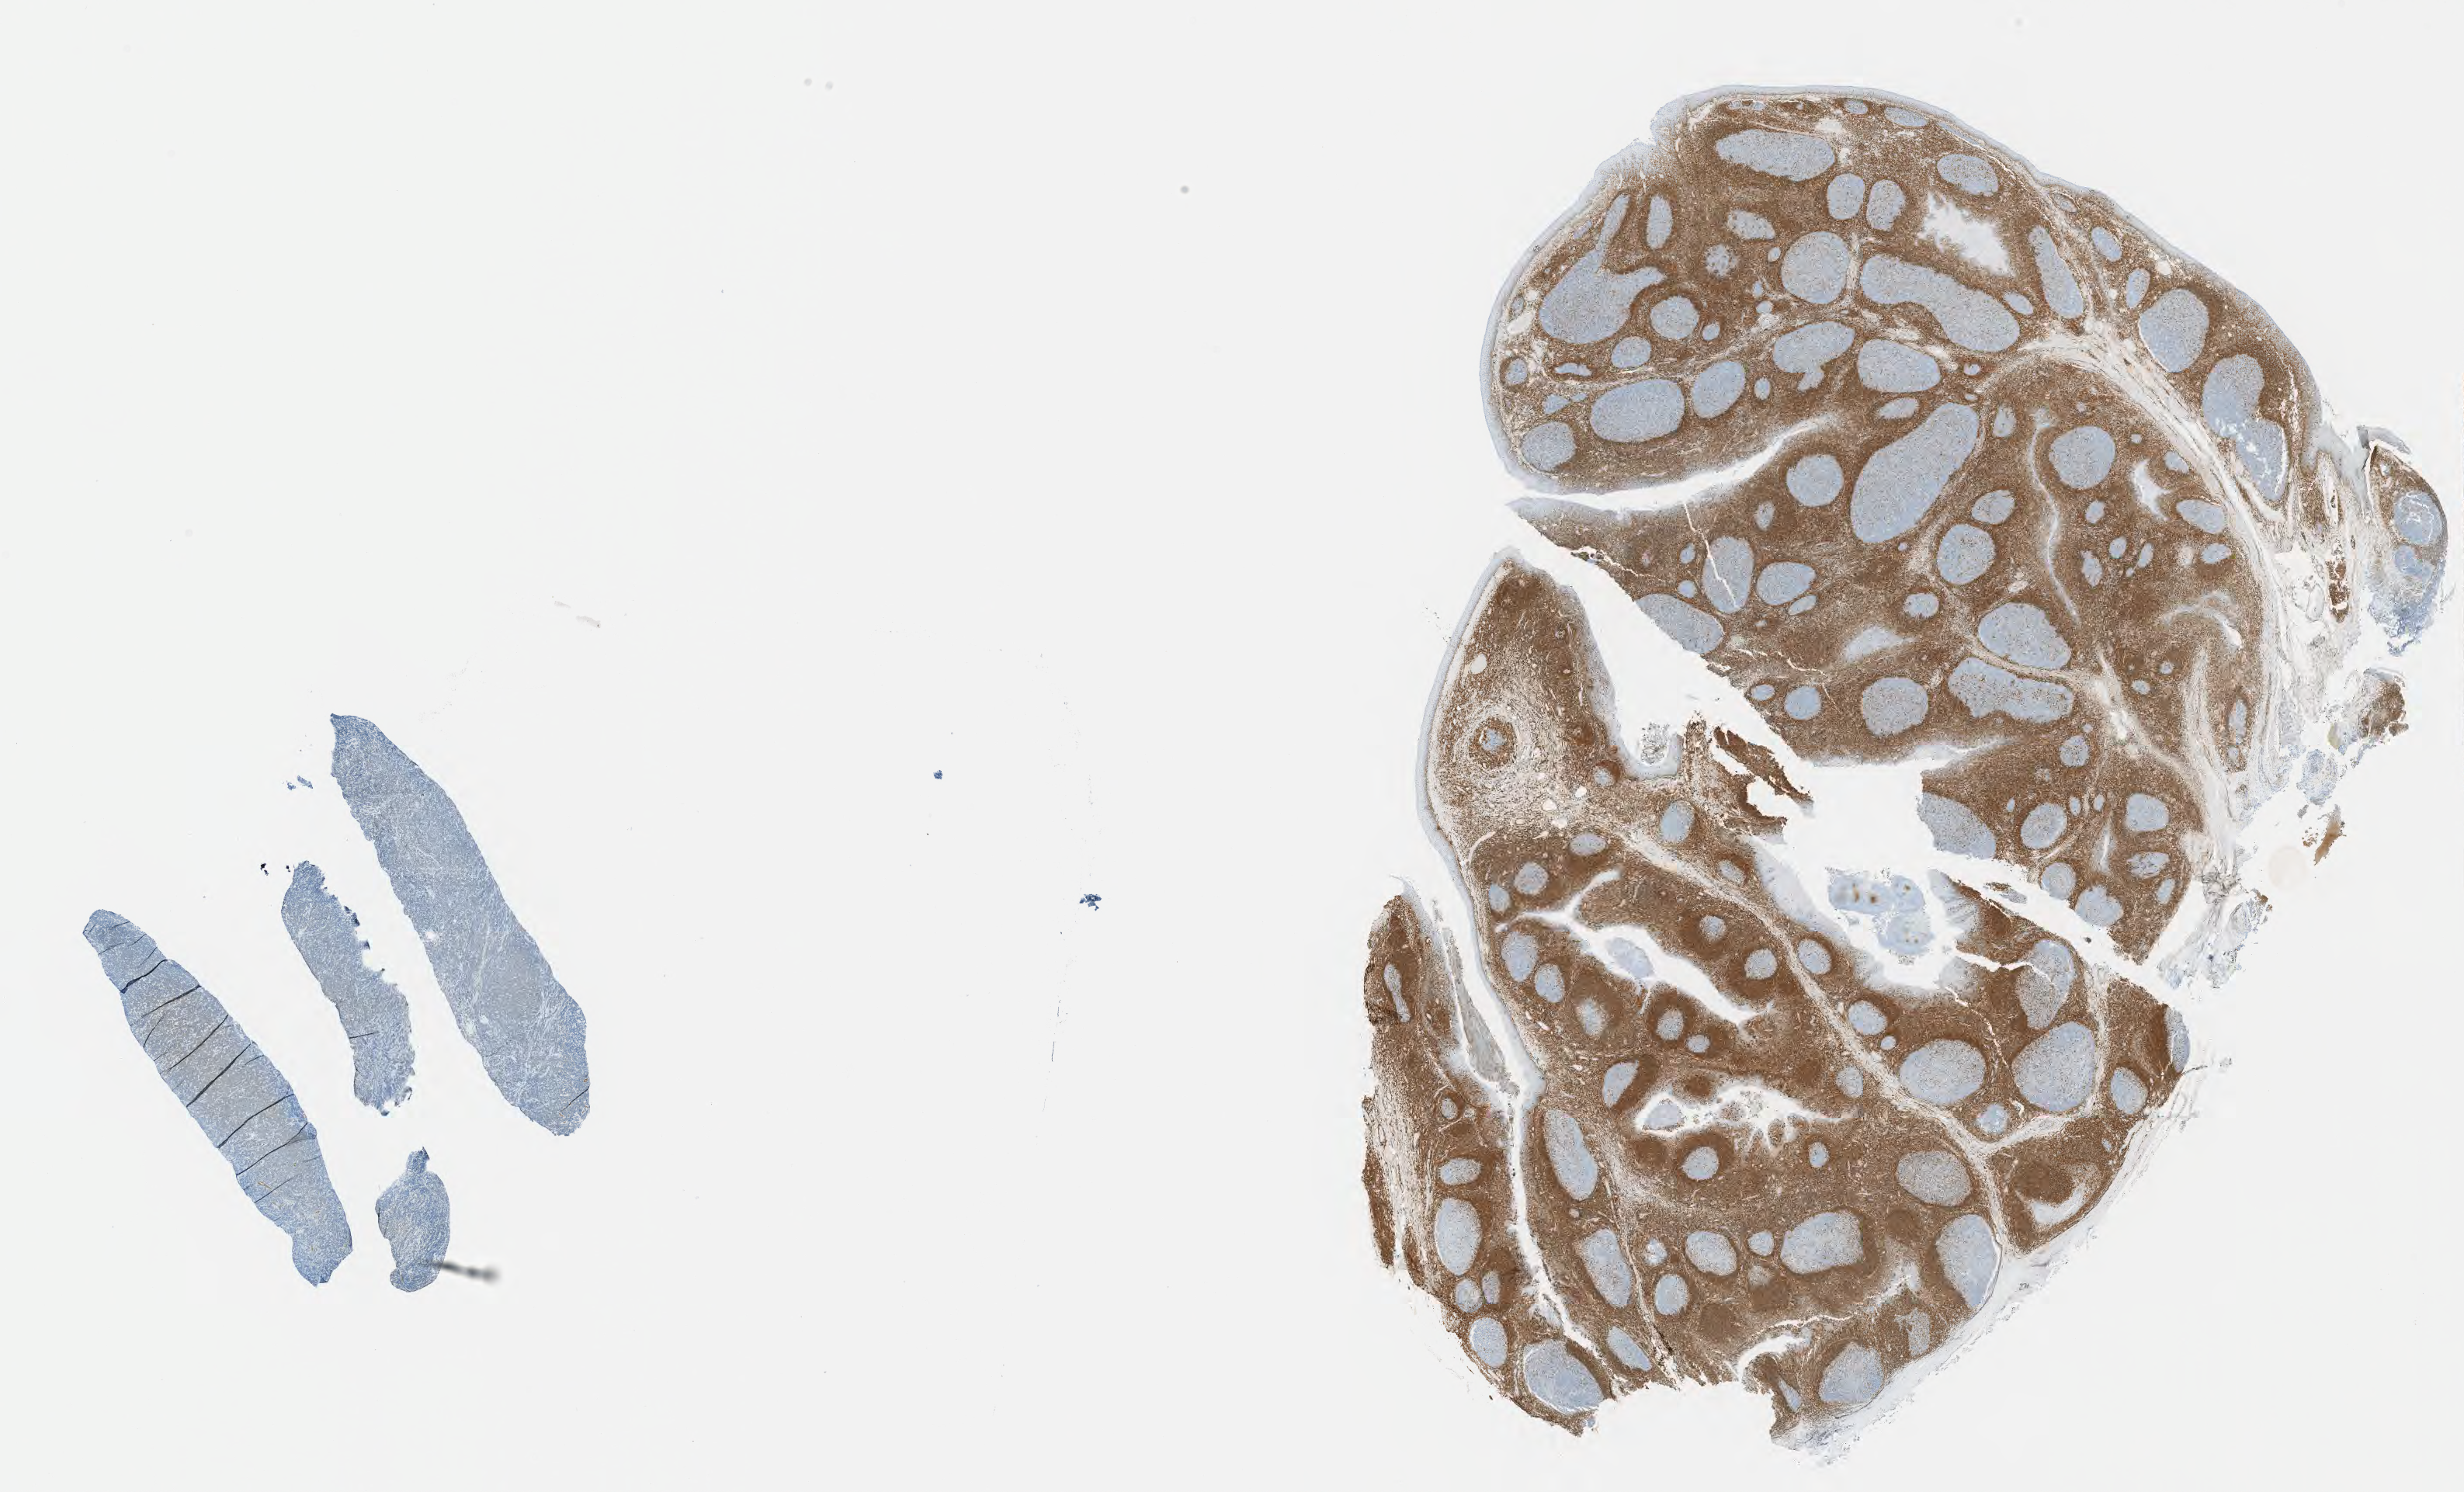
IHC for BCL2, whole-slide image, a low-resolution overview of the entire scanned area, about 25.7 x 15.5 mm. Specimen: tumor tissue. Female patient, 46 years old.
Histologic diagnosis: Burkitt lymphoma, NOS.